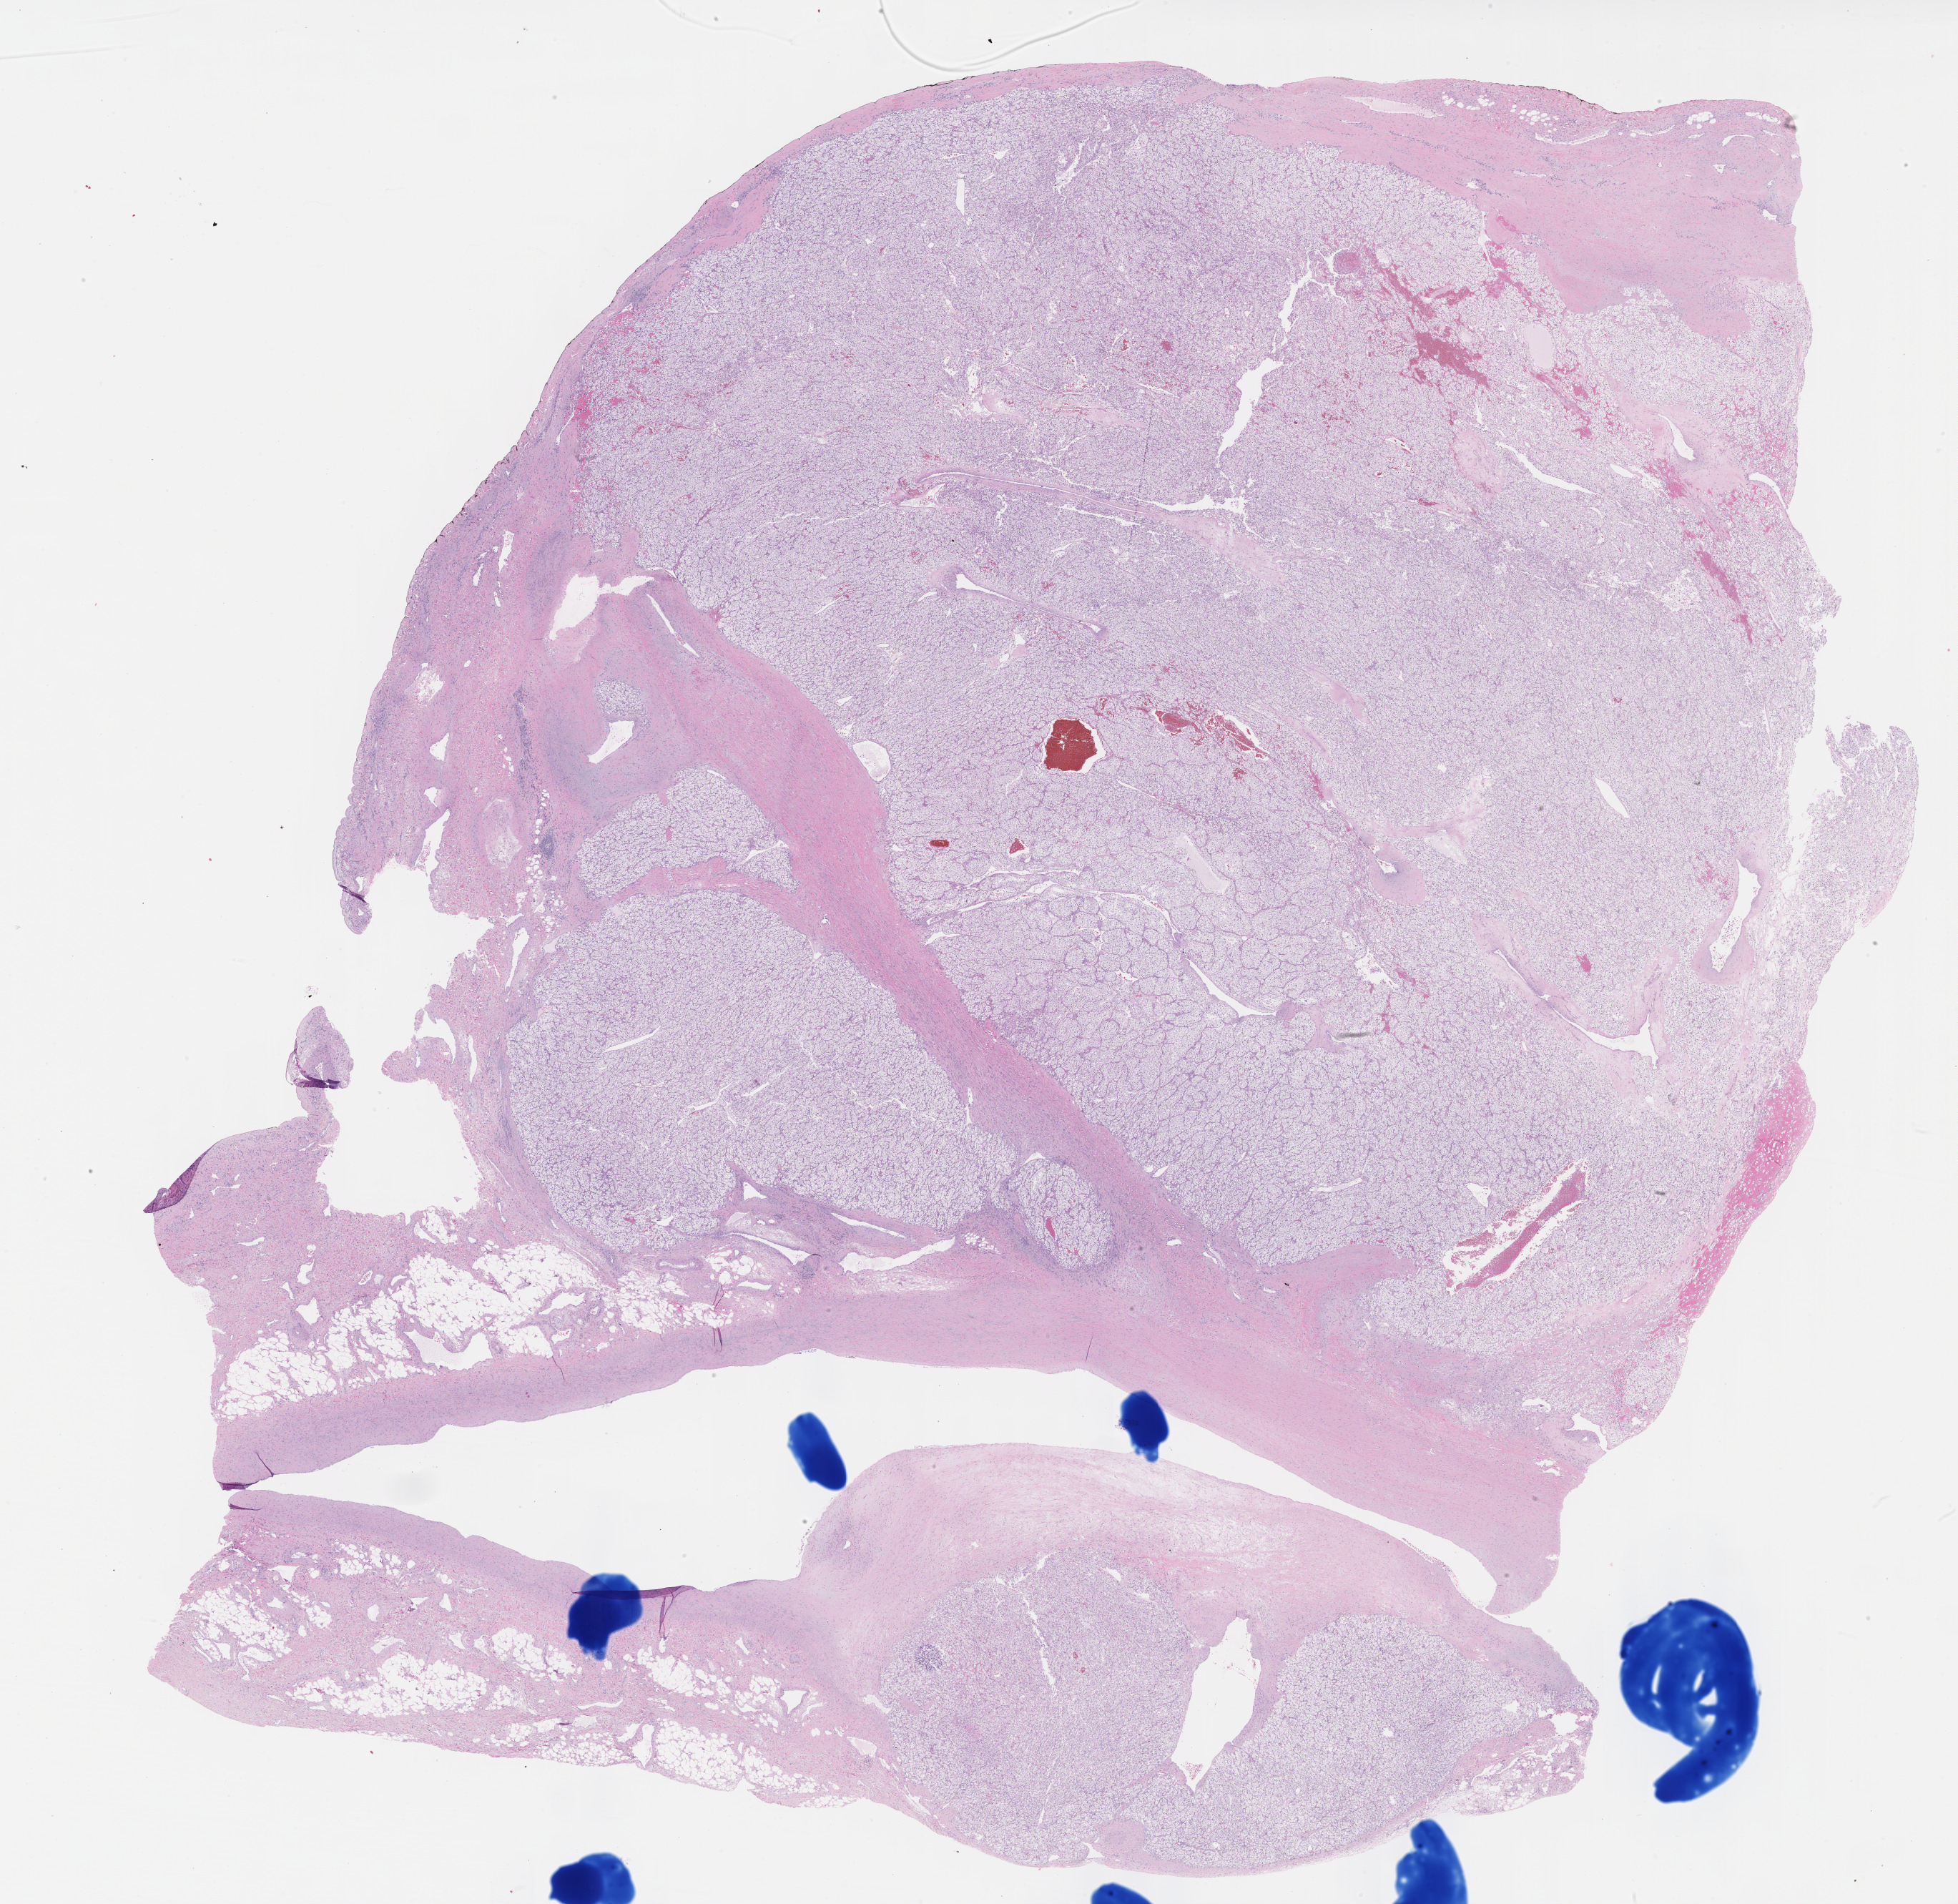
H&E-stained whole-slide image, low-resolution overview of the scanned area, about 22.1 x 21.5 mm, formalin-fixed paraffin-embedded (FFPE) diagnostic section, primary tumour sample from the kidney. Patient: female, age at initial diagnosis 79 years. Histologic grade: G3 (poorly differentiated).
- pathologic diagnosis: Clear cell adenocarcinoma, NOS
- laterality: right
- TNM: T3a NX M0
- AJCC pathologic stage: III (7th edition)